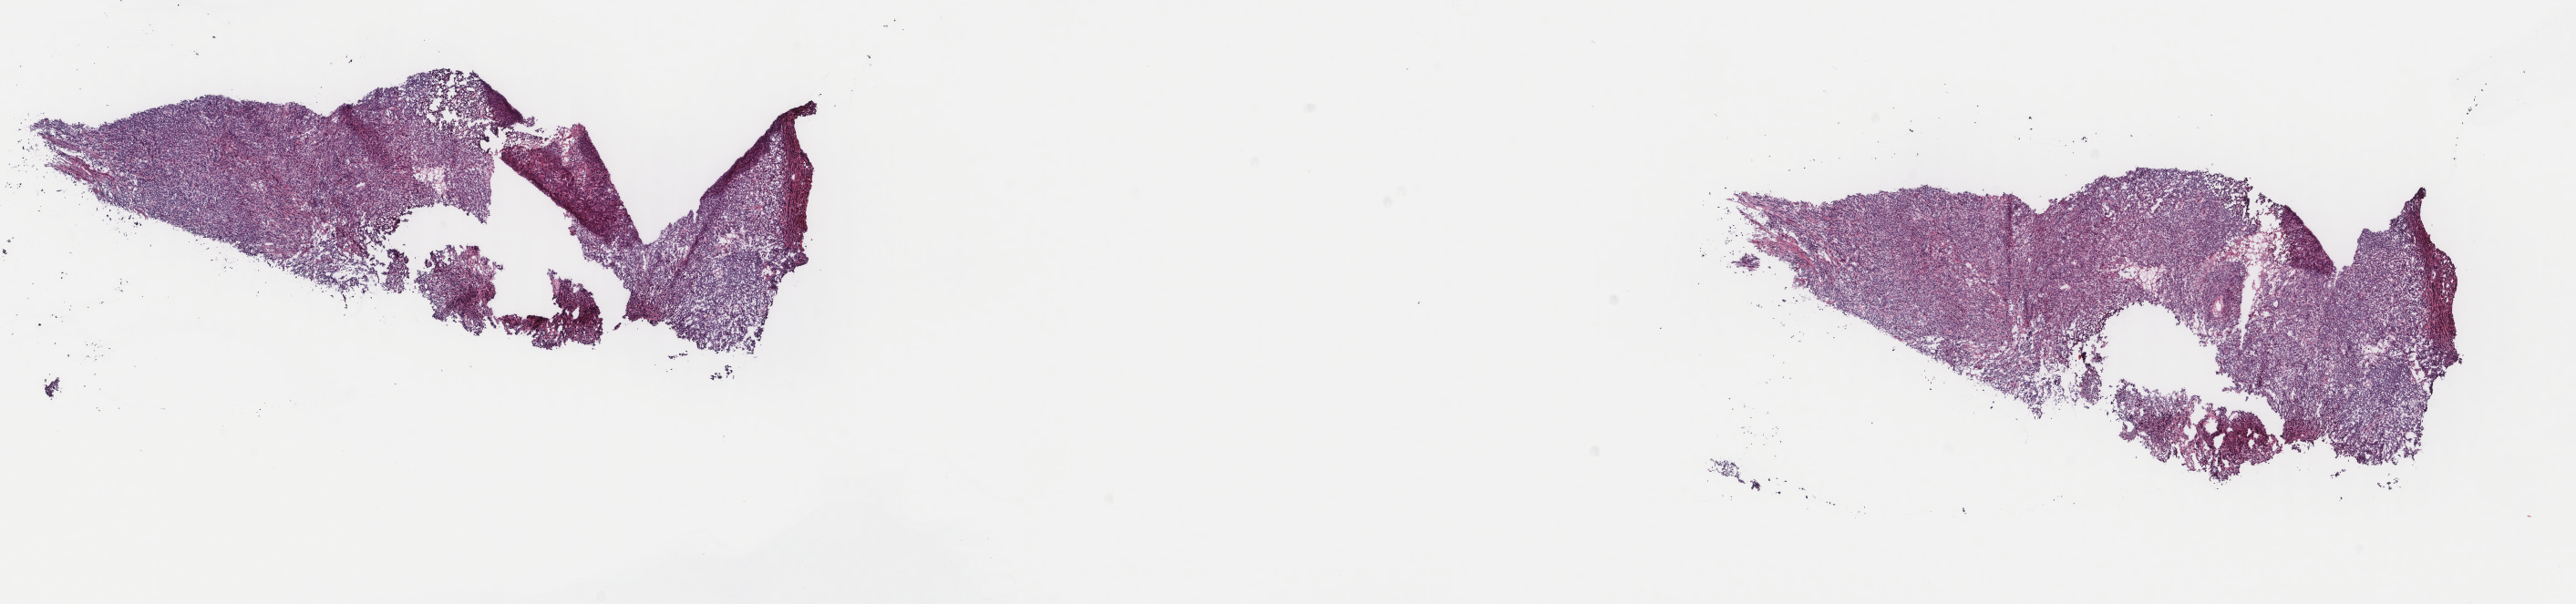
Hematoxylin and eosin (H&E) stained whole-slide image — whole scanned area (about 22.4 x 5.3 mm) shown as a low-resolution overview. Frozen section. Primary tumour sample from the uterus. Female patient. Slide review estimates, as recorded: tumour cells 95%, tumour nuclei 80%, normal cells 0%, stromal cells 0%, necrosis 5%. Infiltration values recorded for this section: lymphocyte infiltration 2%, monocyte infiltration 0%, neutrophil infiltration 0%.
• FIGO stage: IC
• histologic diagnosis: Mullerian mixed tumor (endometrium)